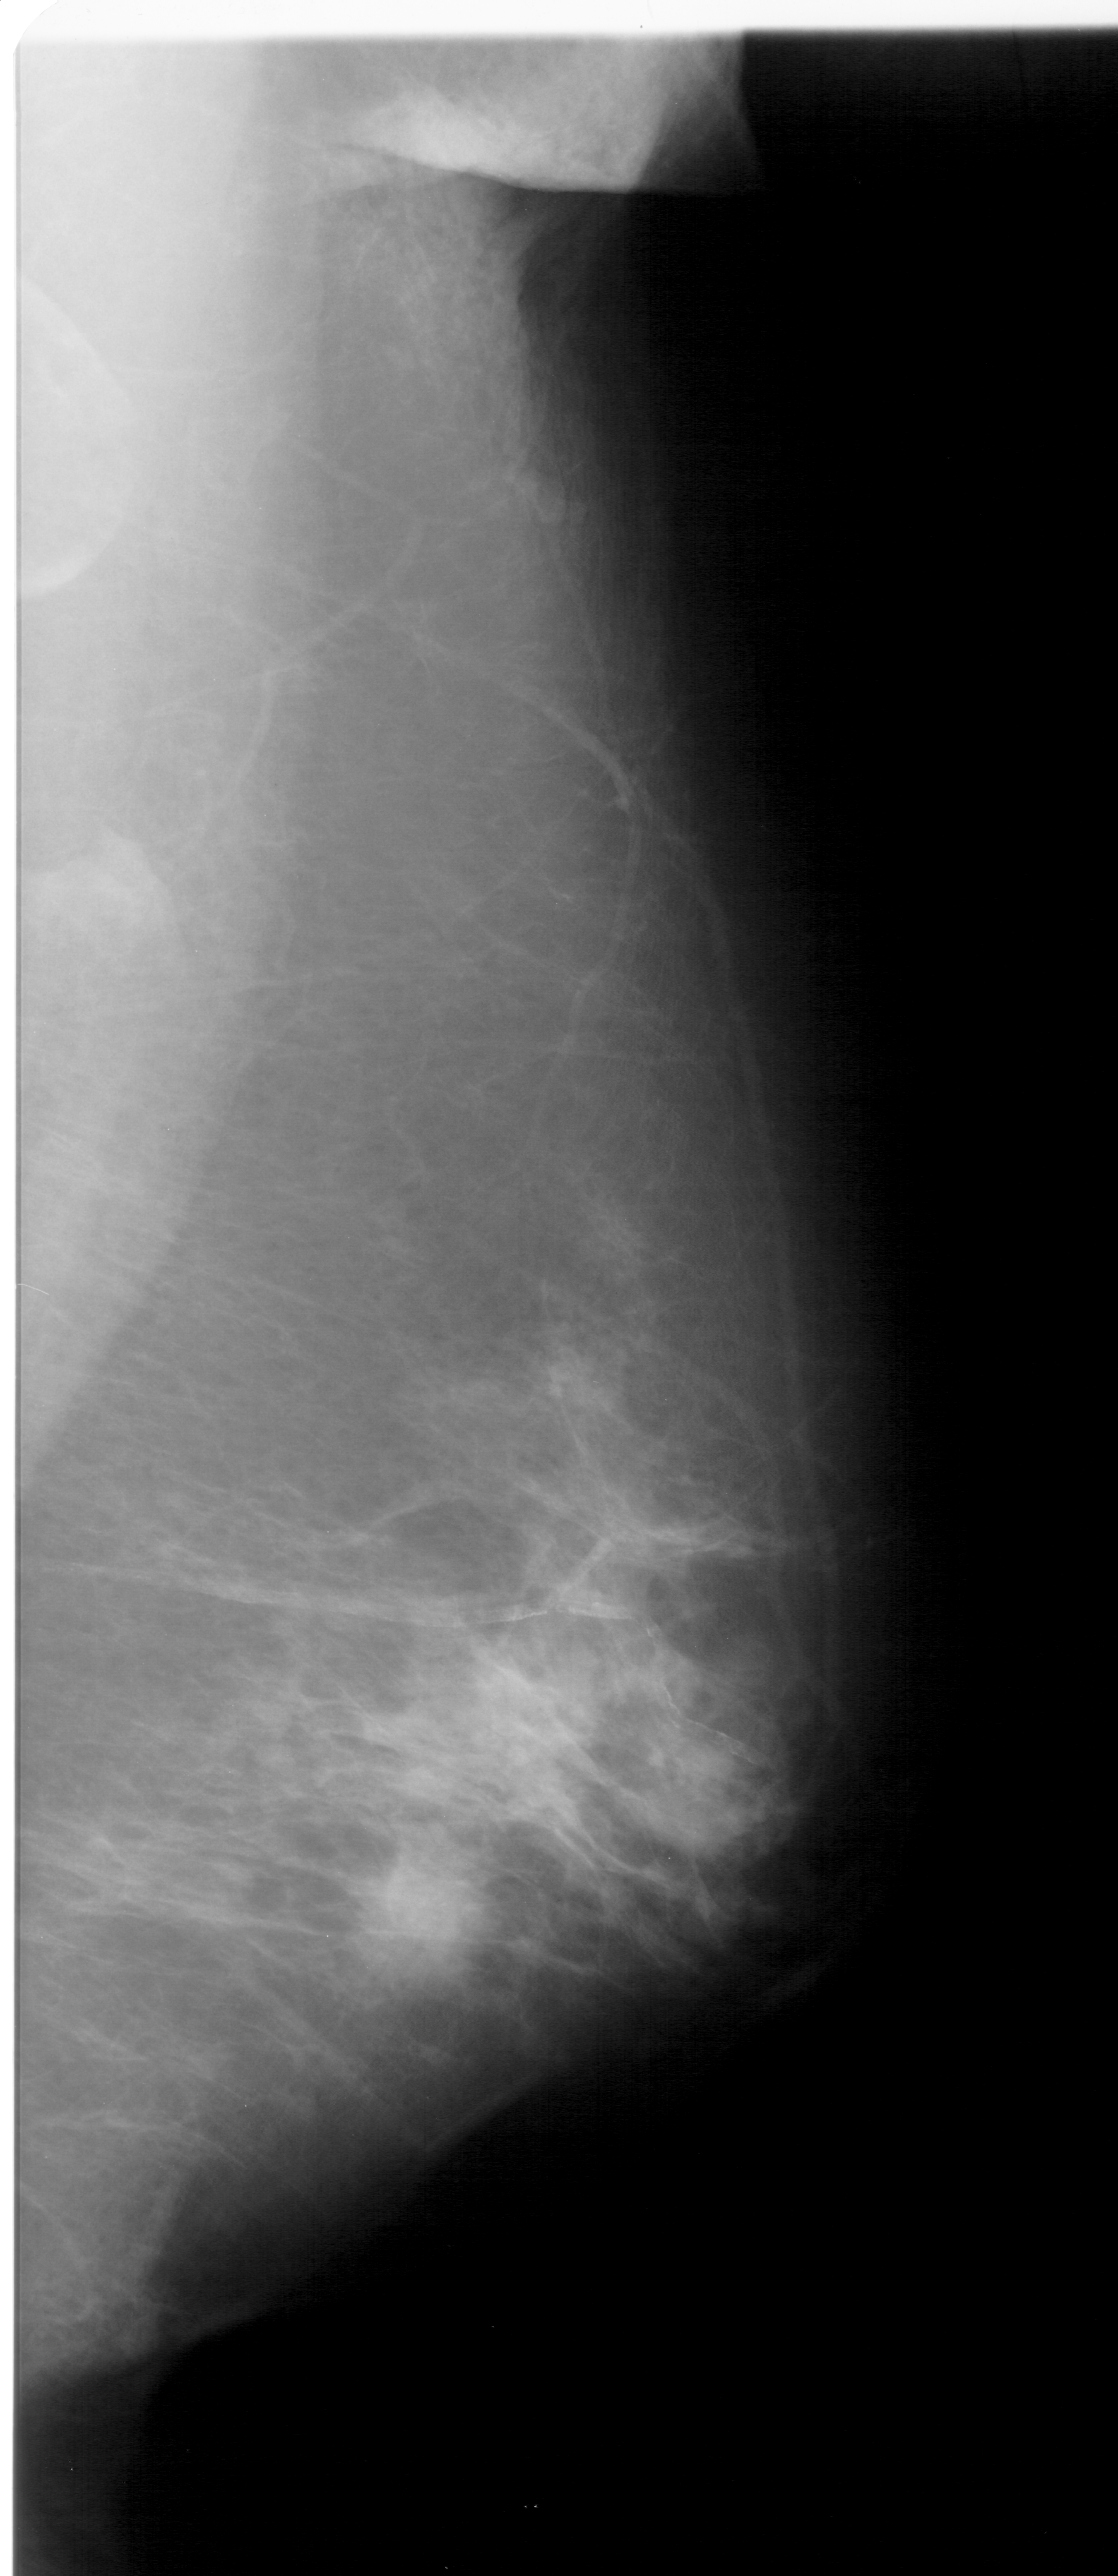
Scanned film-screen mammogram, right breast, mediolateral oblique (MLO) view, breast composition: heterogeneously dense (BI-RADS density category 3 of 4).
Marked findings (only marked abnormalities are described; nothing is implied about the rest of the image): calcifications, morphology pleomorphic, distribution clustered; BI-RADS assessment category 5; subtlety rating 4 on a 1 (subtle) to 5 (obvious) scale; pathology (as recorded): malignant.